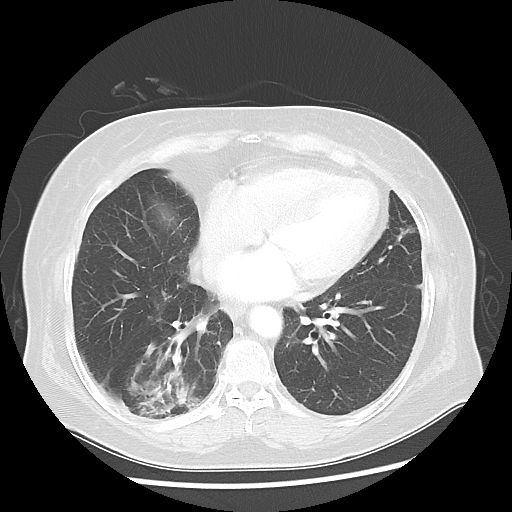
Chest CT, one axial slice. Slice 21 of 56 in the series (ordered by position). Reconstruction kernel LUNG. 120 kVp. Lung window (W 1500 / L -600 HU). 512 × 512 image matrix, field of view 360 × 360 mm. Patient: female, 64 years. From the clinical record (not read from this slice): clinical TNM (as recorded): Tis N0 M0.
Outlined on this slice (bounding box drawn by a radiologist):
- lung tumour (recorded histology: adenocarcinoma): bounding box <126,346,199,430> (left, top, right, bottom; pixels)